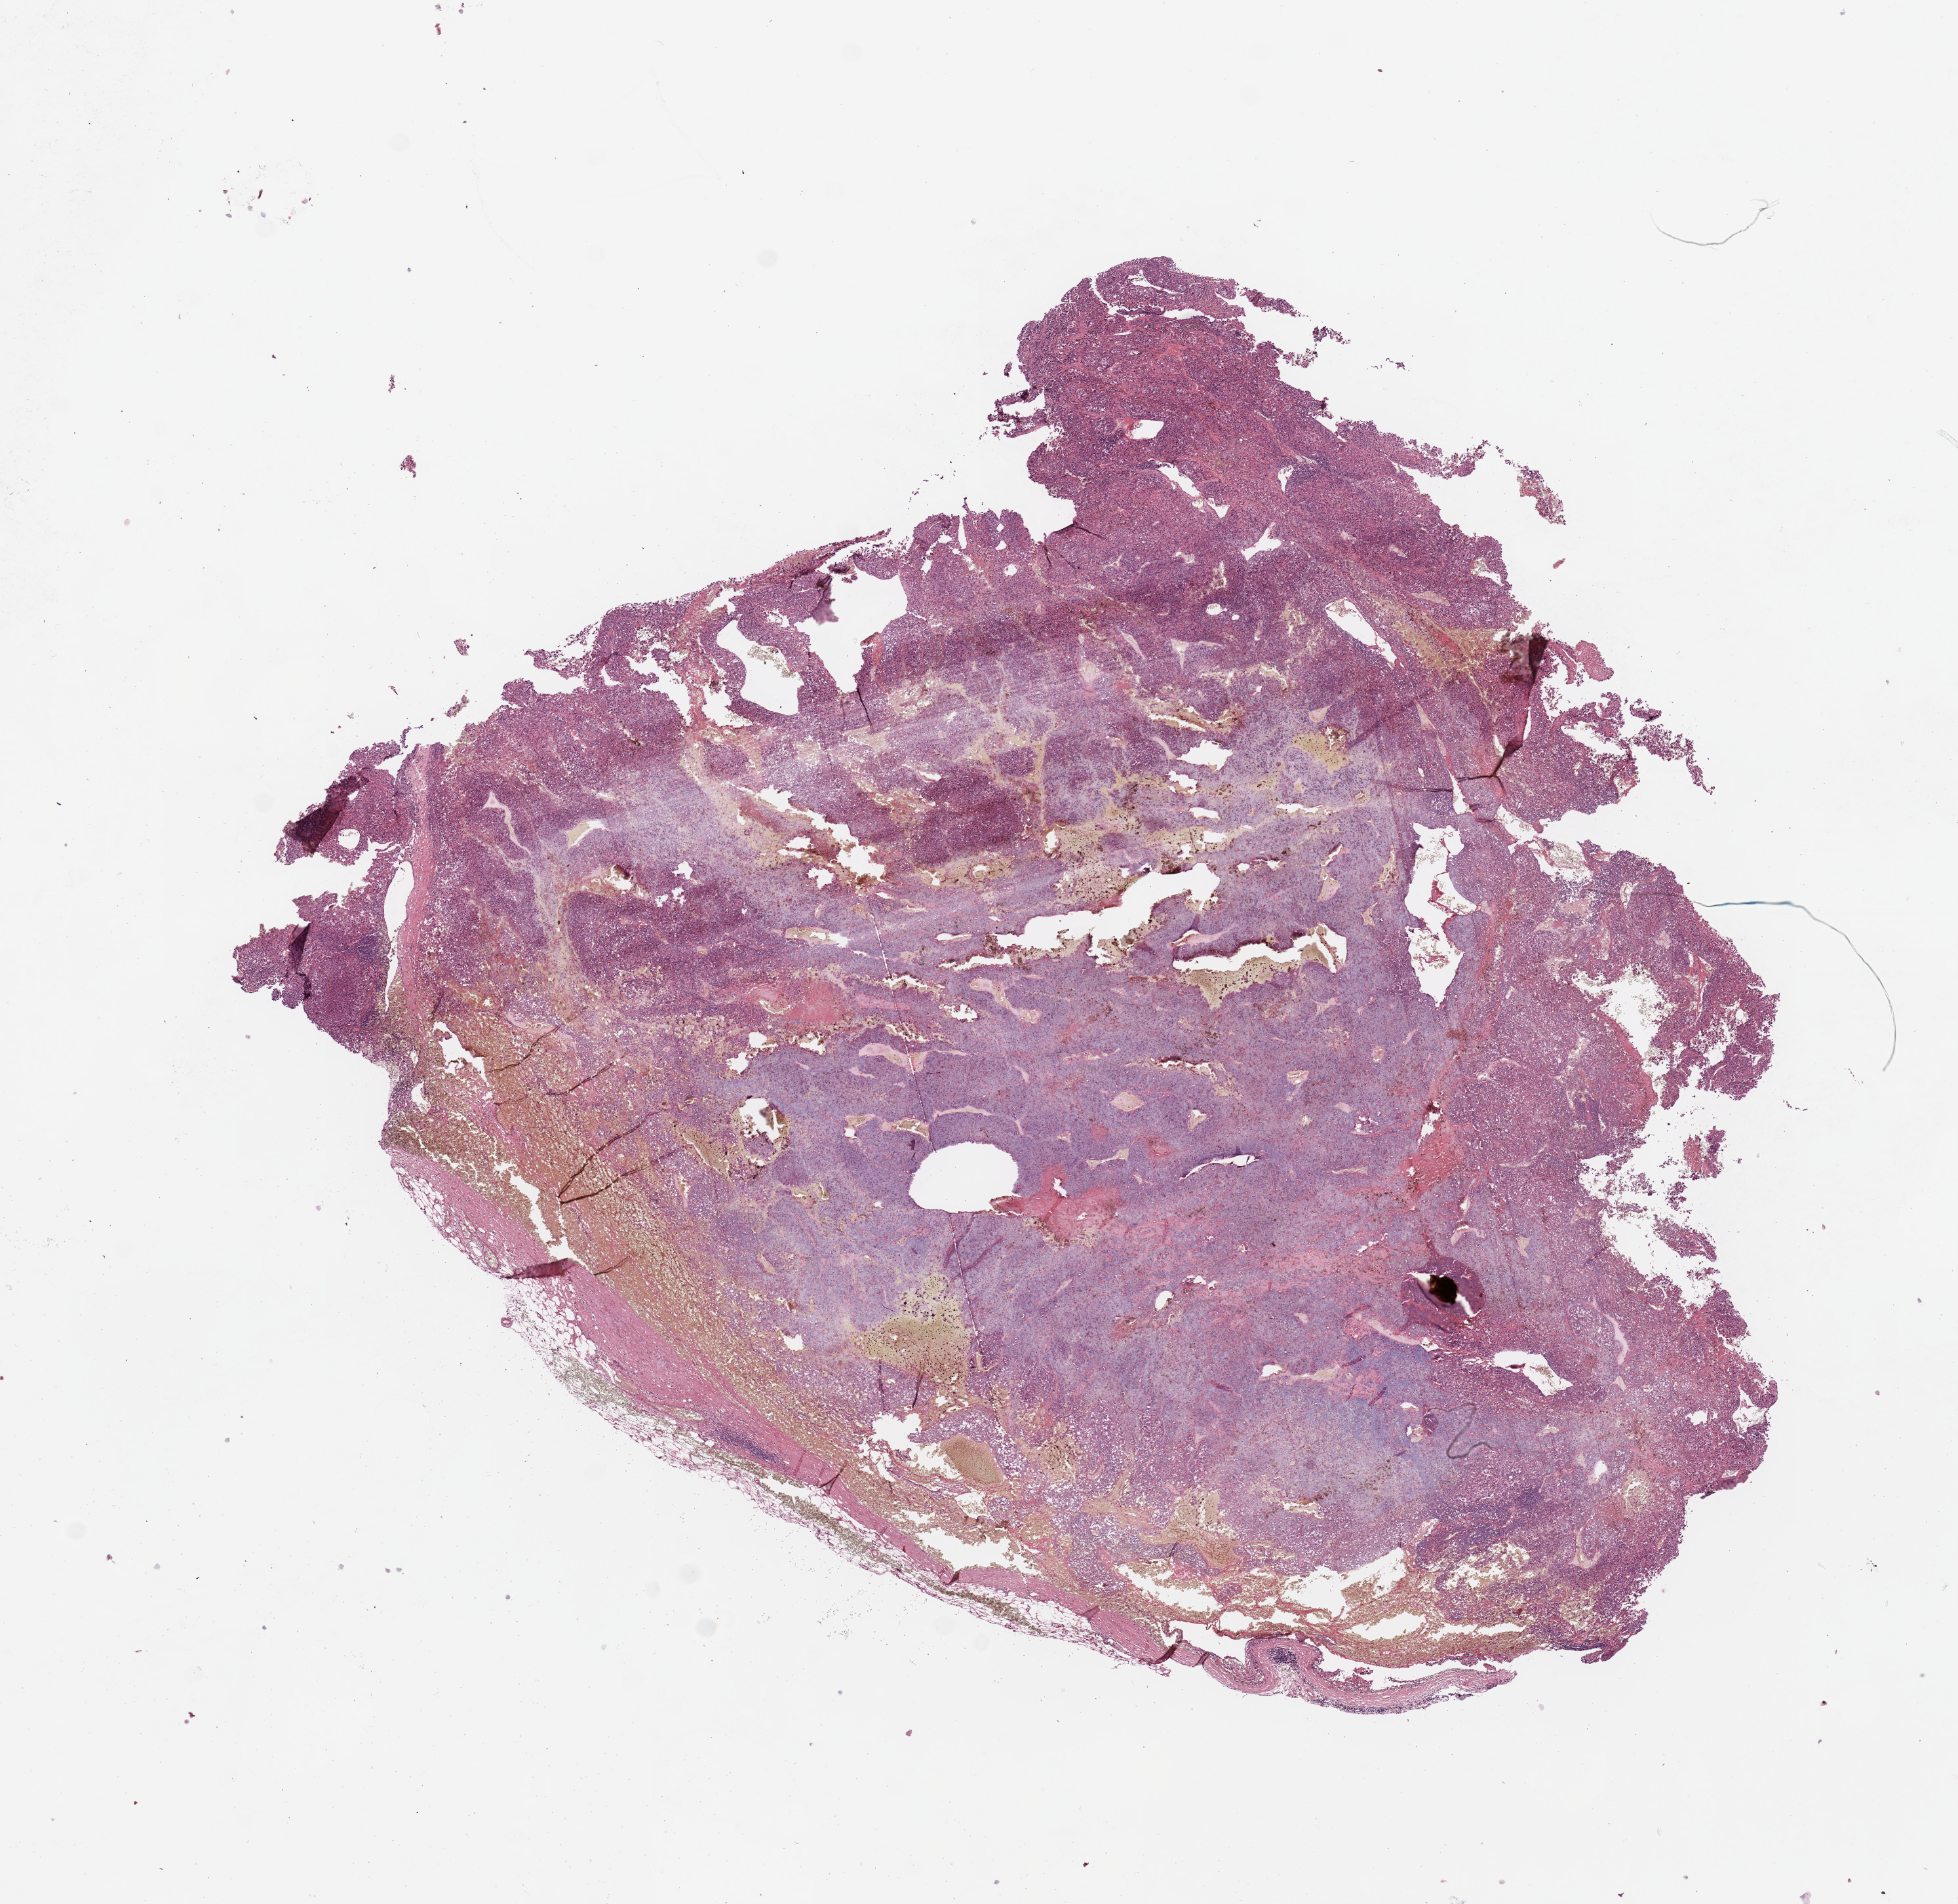
H&E-stained whole-slide image, low-resolution overview of the scanned area, about 11.8 x 11.5 mm (acquisition: 20x scan), melanoma tumour tissue; sampled site not recorded. Male, 60 y/o.
Patient diagnosis (cohort enrolment): cutaneous melanoma (skin).